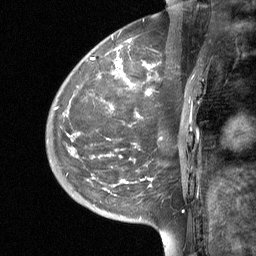
Breast MRI (dynamic contrast-enhanced), one sagittal slice. Position 12 of 64 along the scan axis. Dynamic contrast-enhanced study with each time point stored as its own series, time point 2 of 3 at this slice position (early post-contrast, ordered by acquisition time). 1.5 T. TE 4.8 ms, TR 27 ms. 2 mm slice thickness. 256 × 256 image matrix, field of view 200 × 200 mm. Female patient, age 42 years. Case-level facts recorded for this patient, not image findings: setting: breast cancer imaged before/during neoadjuvant chemotherapy; receptor status: triple-negative.
Structures marked on this image (semi-automatically segmented with operator editing):
- analysis volume of interest (the breast-tissue region the enhancement analysis was run in; not a lesion): bounding box (x1, y1, x2, y2) in pixels: (46, 29, 203, 190)
- tumour enhancement mask (voxels above the 90 % enhancement threshold inside the analysis volume of interest): (91, 38, 191, 186)